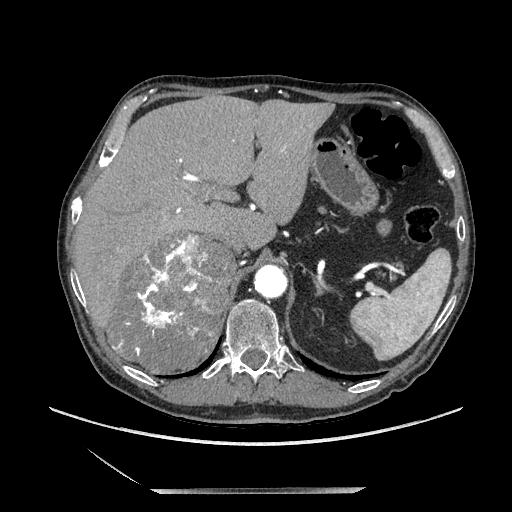
Contrast-enhanced abdominal CT, one axial slice. Position 151 of 243 along the scan axis. Soft-tissue window (W 400 / L 40 HU). 512 × 512 image matrix, field of view 420 × 420 mm. Male patient. From the clinical record (not read from this slice): diagnosis: adrenocortical carcinoma; tumour side: right adrenal; tumour size at pathology: 16 cm.
Structures marked on this image (semi-automatic segmentation, software-assisted and operator-edited):
- mass: bounding box (x1, y1, x2, y2) in pixels: (110, 236, 235, 373)